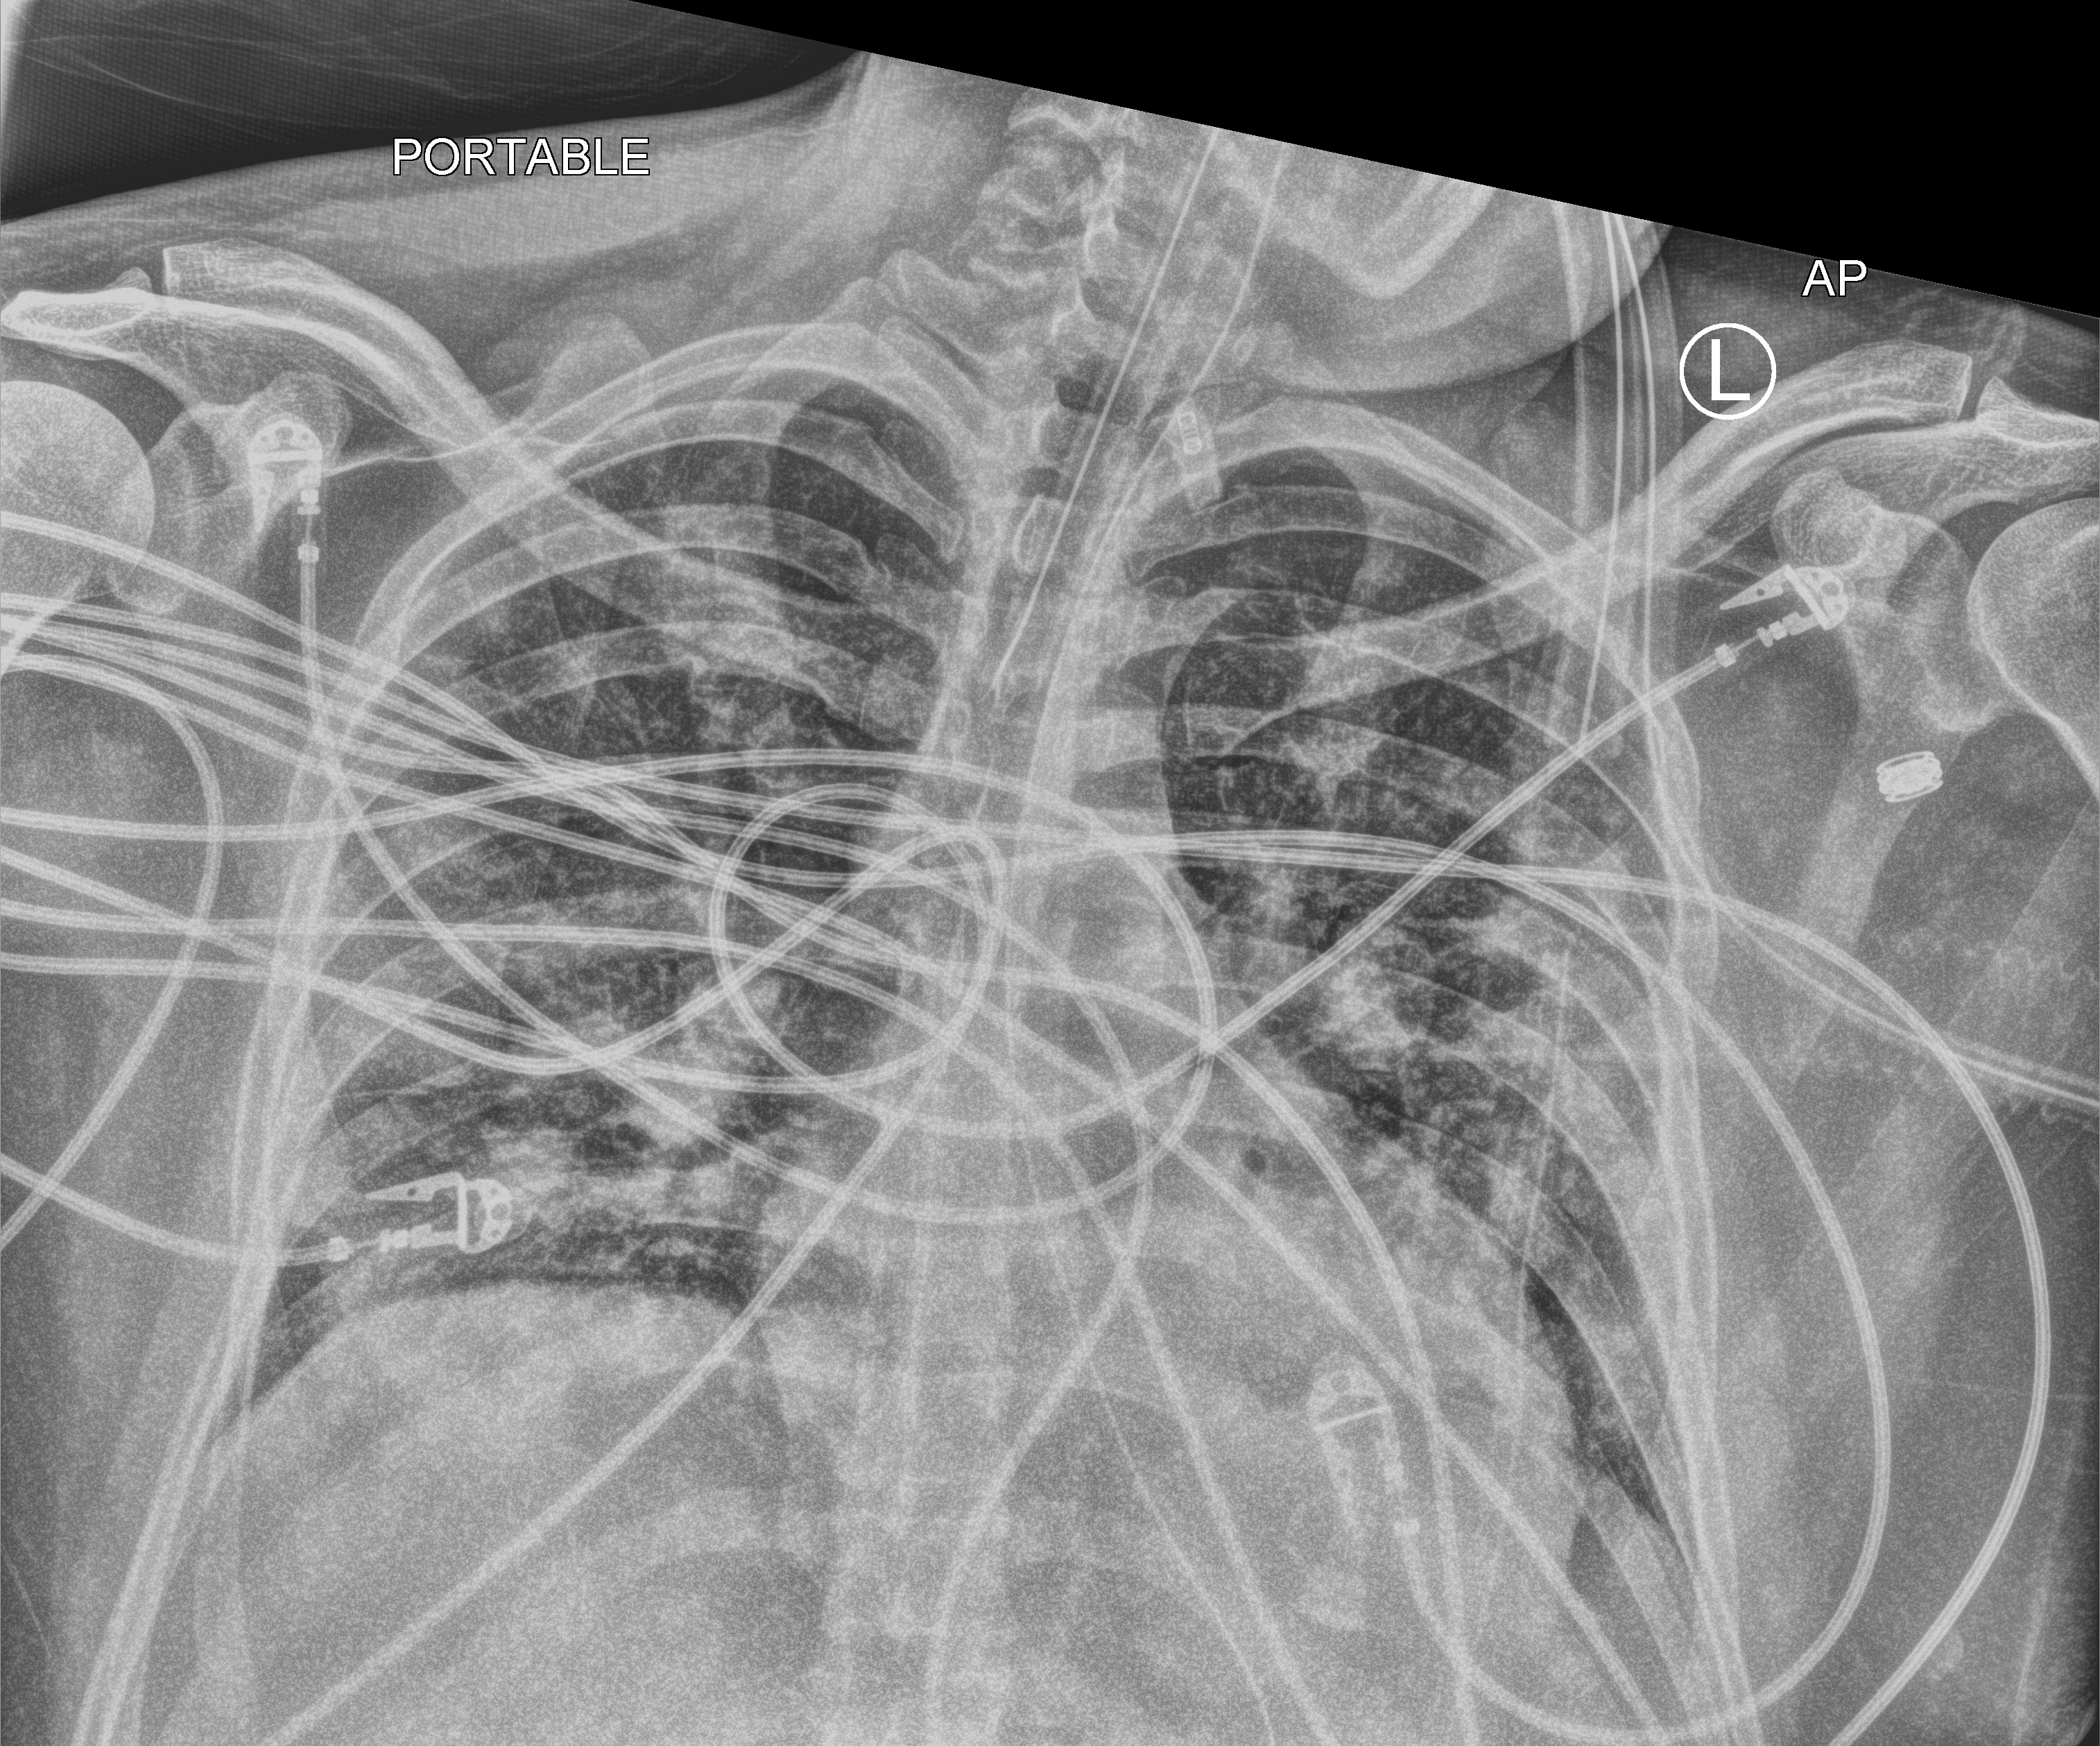
Portable chest radiograph, anteroposterior (AP) projection. Patient hospitalised with COVID-19; male, aged 18–59 years.
Admission-level facts for this patient (not findings on this image; timing relative to this image not recorded):
- mechanically ventilated during this hospital stay: yes